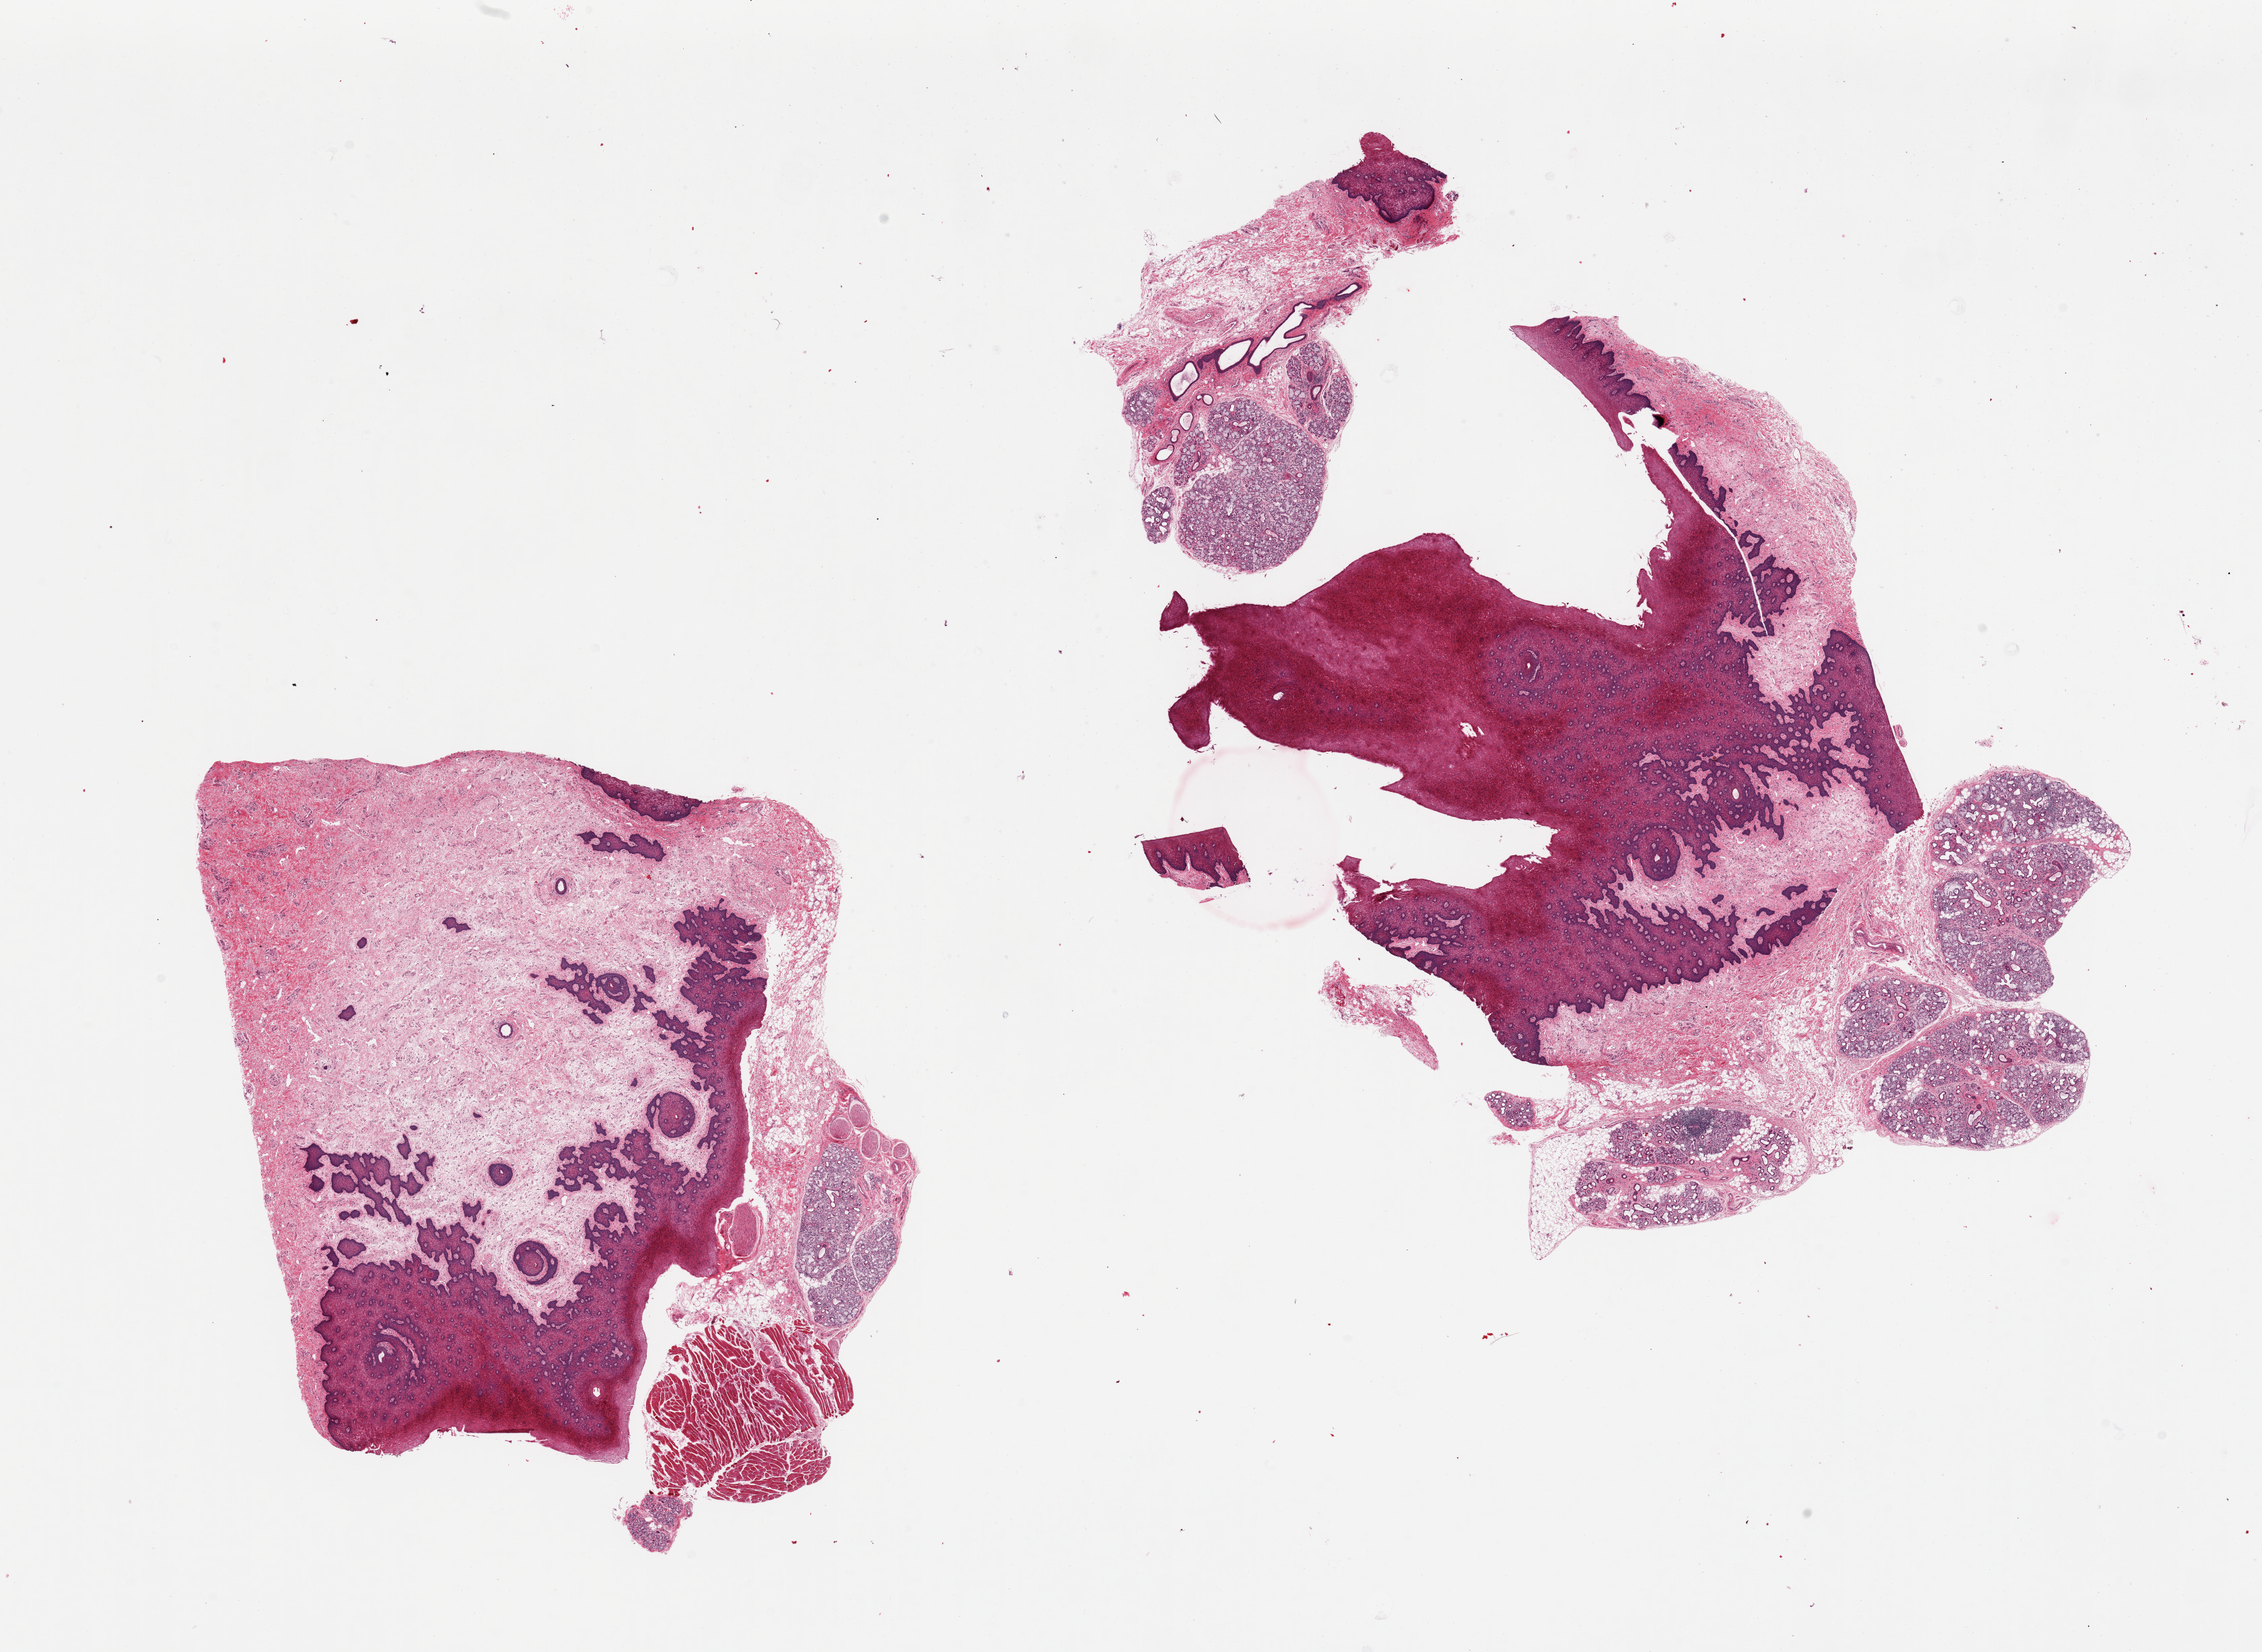
Digitized hematoxylin and eosin (H&E)-stained section, whole scanned area (about 26.6 x 19.4 mm) shown as a low-resolution overview; PAXgene-fixed paraffin-embedded (PFPE) section; target tissue: minor salivary gland; tissue donor sample. Donor sex: female.
Review note (as recorded): 2 pieces, salivary gland elements (~15%), mucosa, stroma, skeletal muscle, and nerve tissue. Acute and chronic sialadenitis.